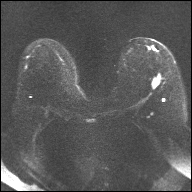
Breast MRI, one axial slice; slice 16 of 32 in the series (ordered by position); diffusion-weighted series; image 2 of 4 stored at this slice position (different b-values; order by instance number); 1.5 T; 4 mm slice thickness; 192 × 192 image matrix, field of view 360 × 360 mm. Female patient.
Outlined on this slice (manually delineated by an expert):
- tumour on diffusion-weighted imaging: bounding box <153,78,160,86> (left, top, right, bottom; pixels)